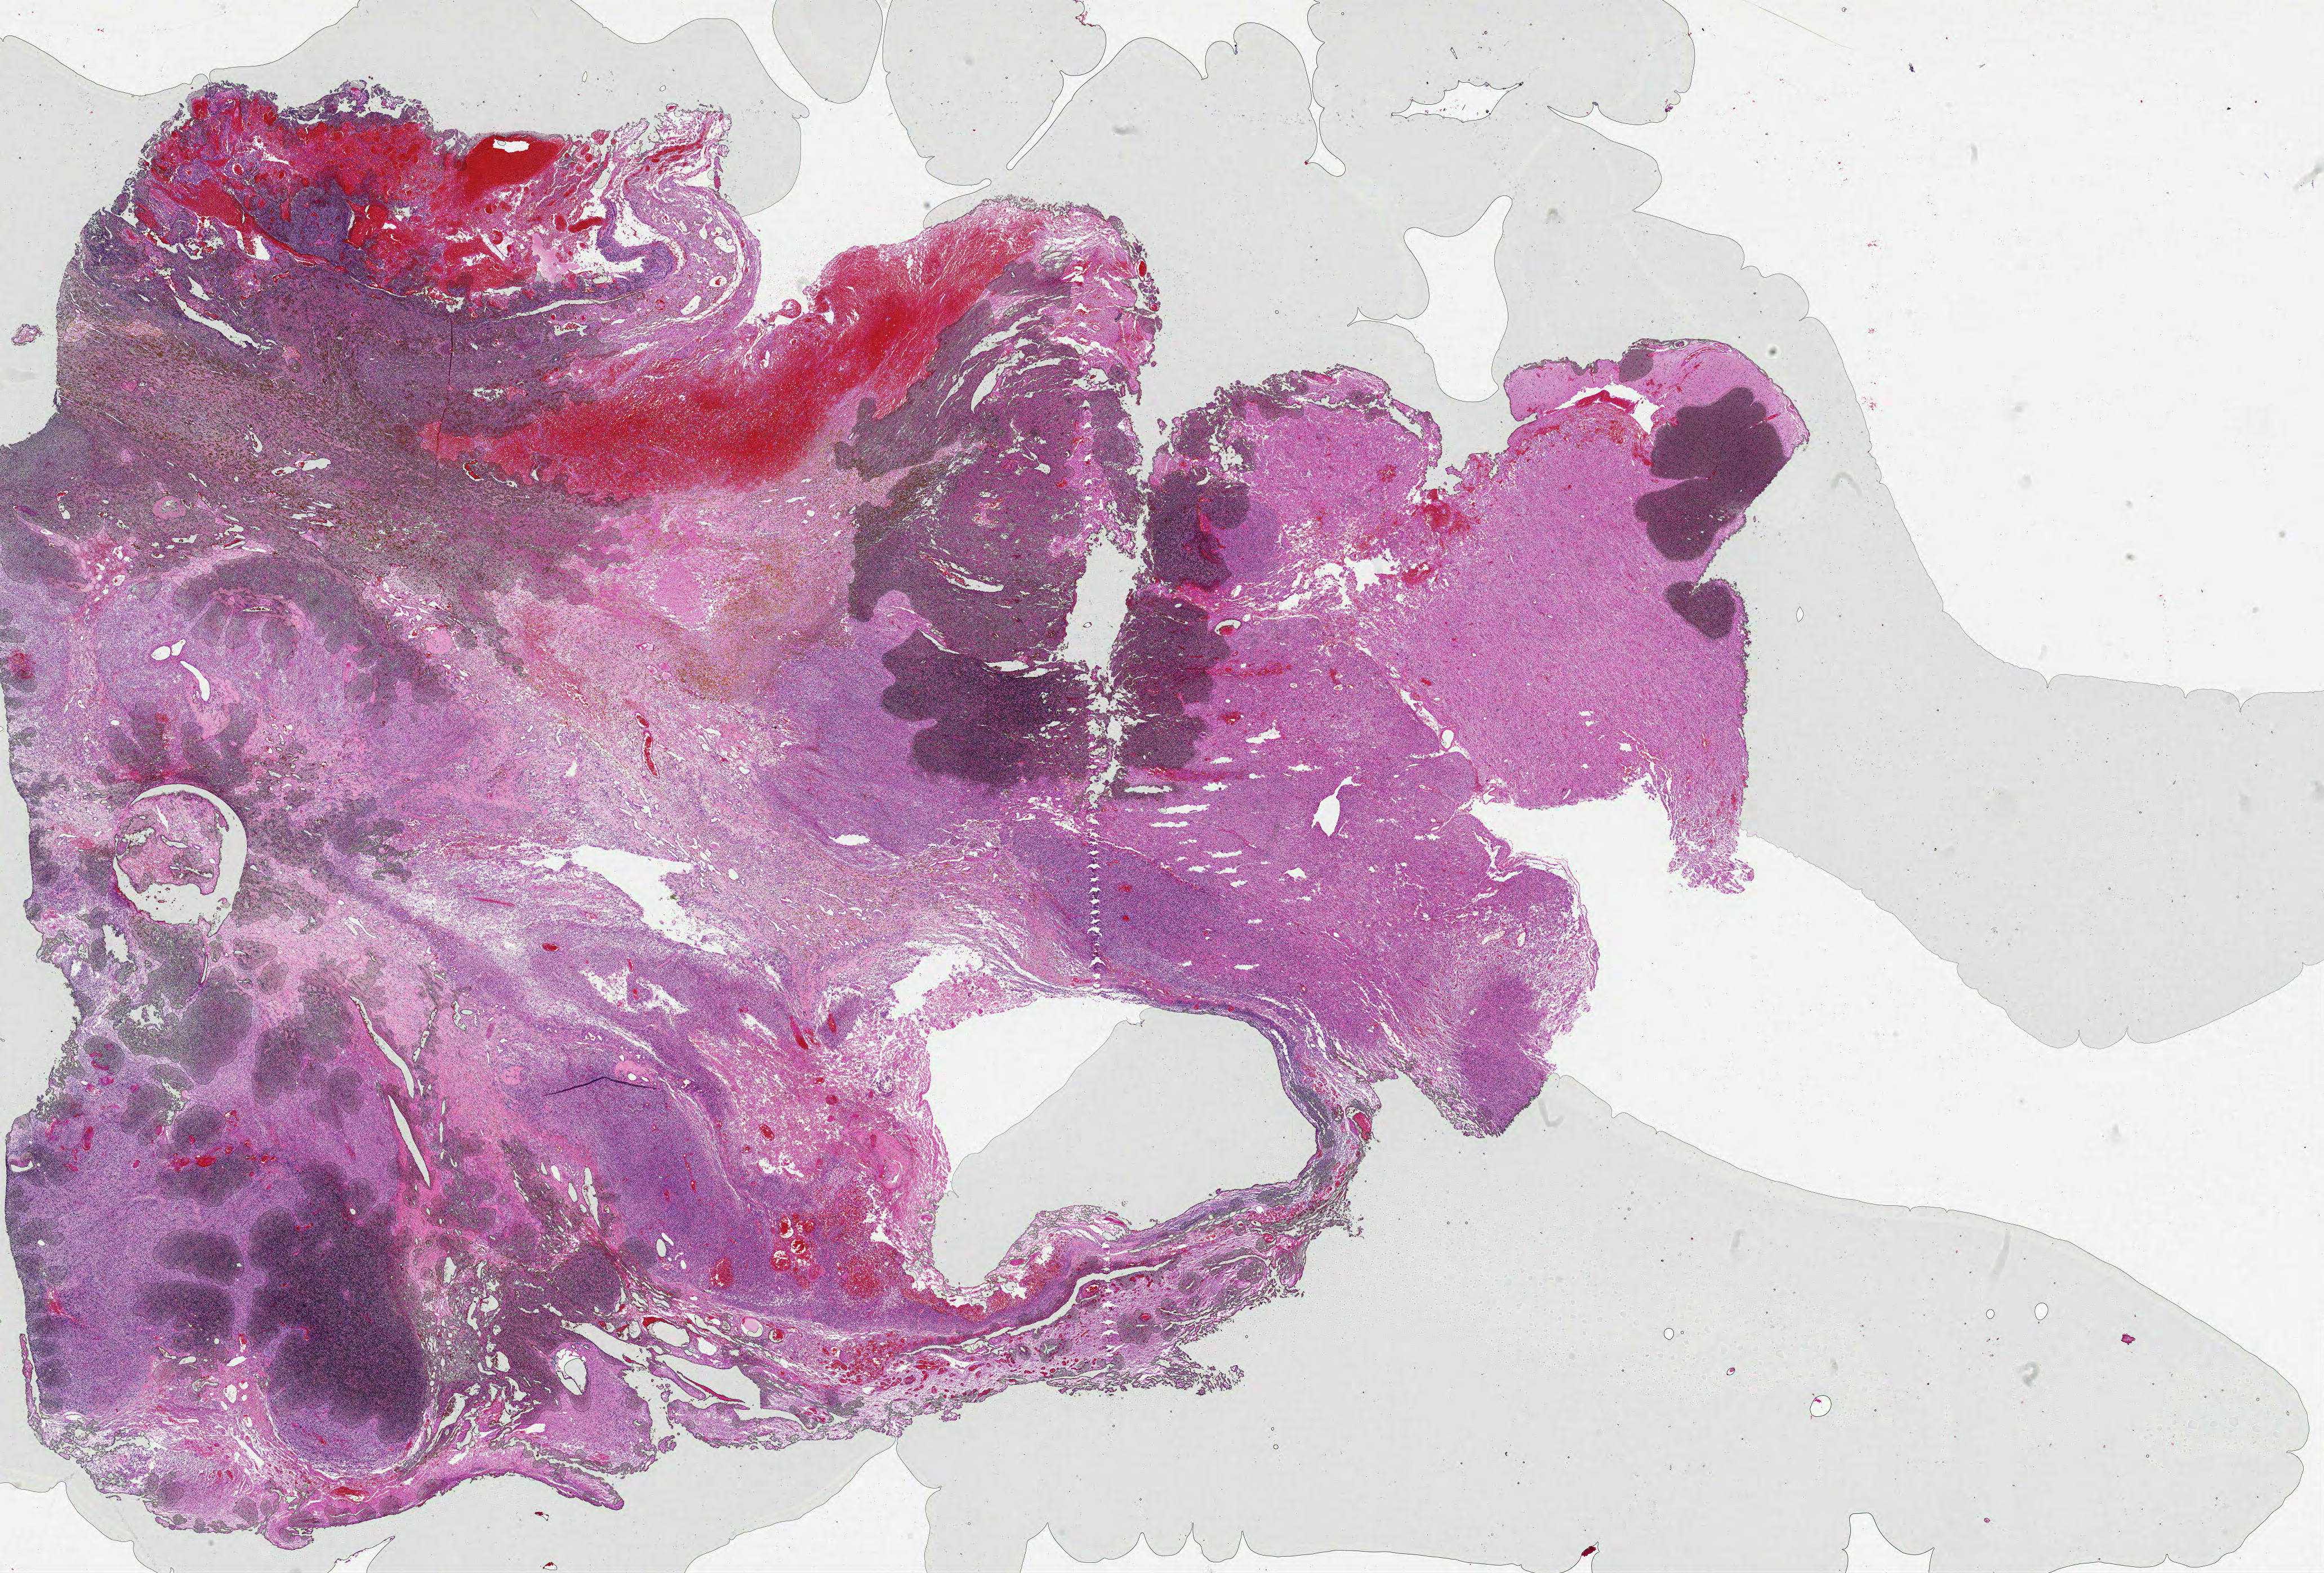
Digitized H&E-stained tissue section (whole slide) — low-resolution overview of the scanned area, about 33.0 x 22.3 mm (slide scanned at 20x); formalin-fixed paraffin-embedded (FFPE) diagnostic section; sample: primary tumour, brain. Male, age 52 years at initial diagnosis.
Pathologic diagnosis: Glioblastoma.